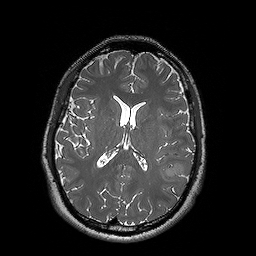
Brain MRI from a brain-tumour surgery series, one axial slice. Slice 77 of 192 in the series (ordered by position). 1 mm slice thickness. 256 × 256 image matrix, field of view 250 × 250 mm. From the clinical record (not read from this slice): histopathology: Oligodendroglioma; WHO grade: 2; IDH mutation: yes.
Structures marked on this image (manually delineated by an expert):
- tumour: bounding box (x1, y1, x2, y2) in pixels: (159, 166, 193, 182)